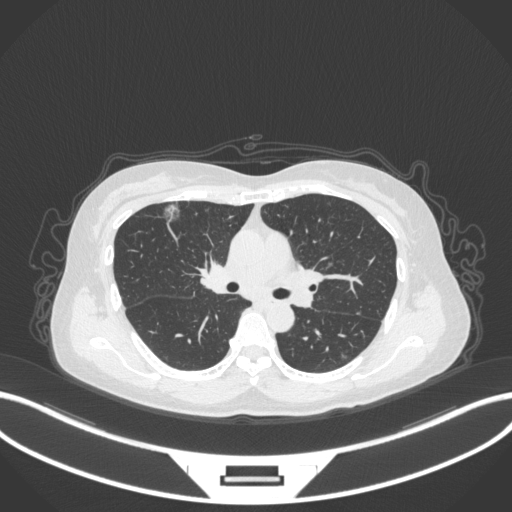
Chest CT, one axial slice; position 199 of 317 along the scan axis; reconstruction kernel B31f; lung window (W 1500 / L -600 HU); 1 mm slice thickness; 512 × 512 image matrix. Female patient, age 61 years. From the clinical record (not read from this slice): clinical TNM (as recorded): T1b N0 M0.
Structures marked on this image (rectangle marked by the reading radiologist):
- lung tumour (recorded histology: adenocarcinoma): box from (x=158, y=202) to (x=181, y=226) px